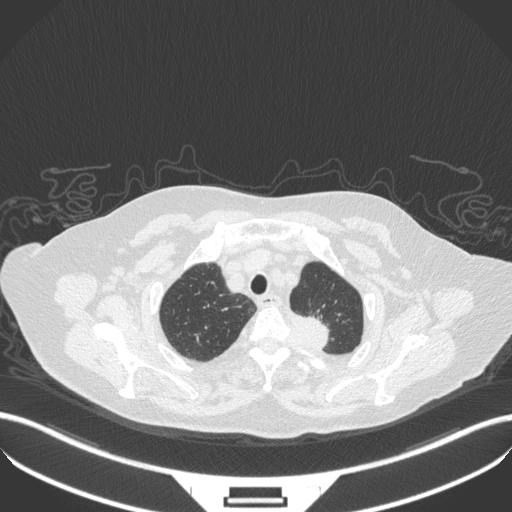
Chest CT, one axial slice; position 296 of 353 along the scan axis; reconstruction kernel B31f; lung window (W 1500 / L -600 HU); 1 mm slice thickness; 512 × 512 image matrix, field of view 400 × 400 mm. Patient: female, 81 years. Case-level facts recorded for this patient, not image findings: clinical TNM (as recorded): T2a N0 M0.
Structures marked on this image (bounding box drawn by a radiologist):
- lung tumour (recorded histology: adenocarcinoma): bounding box <290,310,336,352> (left, top, right, bottom; pixels)